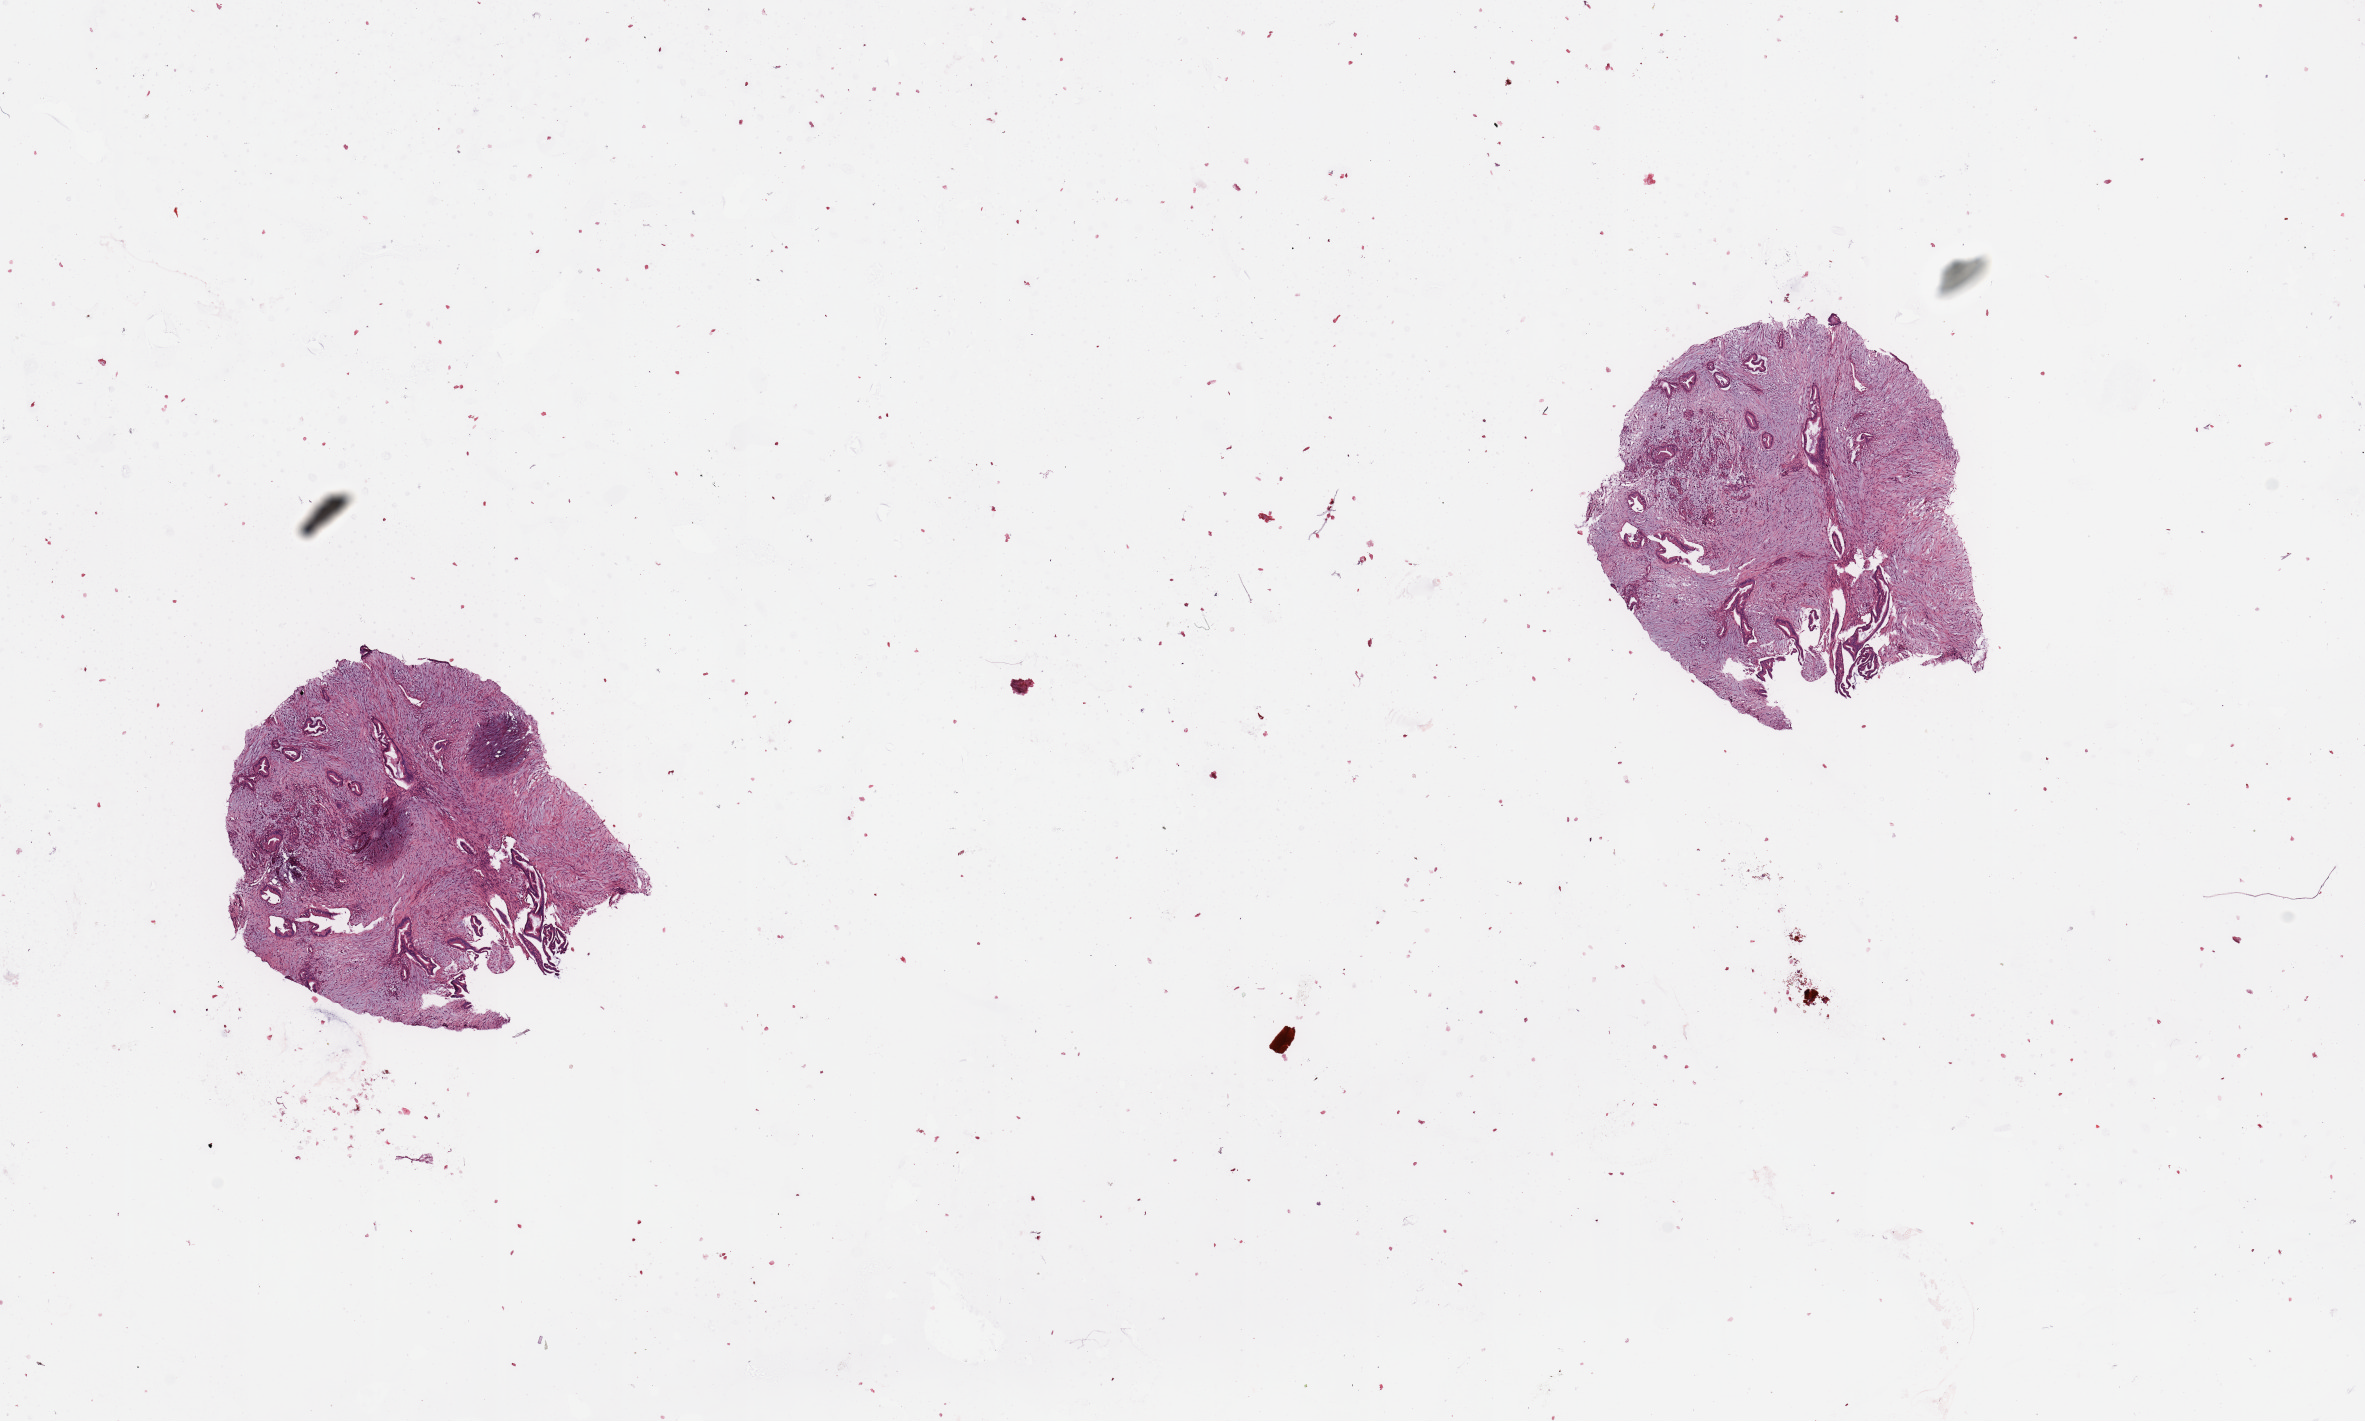
Hematoxylin and eosin (H&E) stained whole-slide image, a low-resolution overview of the entire scanned area, about 18.7 x 11.2 mm, tumour tissue sample, sampled site: pancreas. Patient: female, age 80 years. Histologic grade: G2 (moderately differentiated). Composition of this section per pathologist review: tumour nuclei 40%, necrosis 2%.
Histologic diagnosis: Infiltrating duct carcinoma, NOS. AJCC pathologic stage: III. Primary tumour site (as recorded): head.